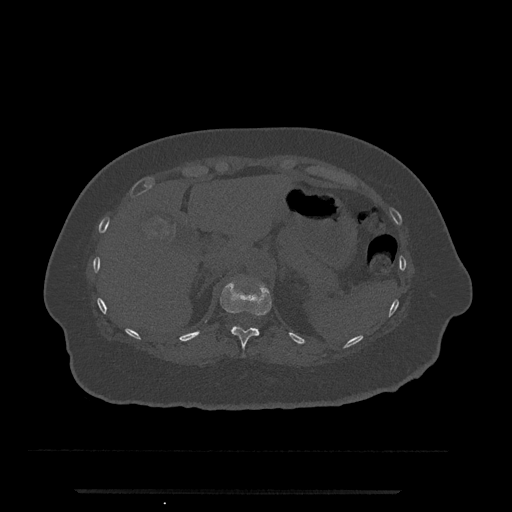
CT including the spine, one axial slice; position 217 of 797 along the scan axis; reconstruction kernel Br40s/3; 120 kVp; bone window (W 1800 / L 400 HU); 0.5 mm slice thickness; 512 × 512 image matrix, field of view 440 × 440 mm. Female patient, age 51 years. From the clinical record (not read from this slice): primary cancer: neuro; vertebrae with lytic lesions (as recorded): T8.
Outlined on this slice (semi-automatically segmented with operator editing):
- T11 vertebra: bounding box [x1, y1, x2, y2] px = [220, 283, 272, 357]